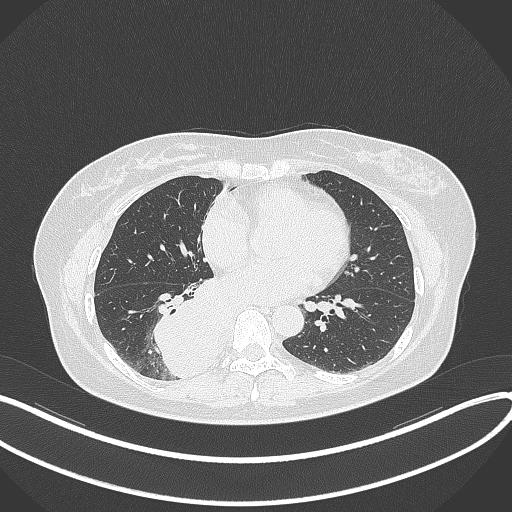
Chest CT, one axial slice. Position 152 of 331 along the scan axis. 120 kVp. Lung window (W 1500 / L -600 HU). 512 × 512 image matrix, field of view 400 × 400 mm. Patient: female, 54 years. From the clinical record (not read from this slice): clinical TNM (as recorded): T4 N0 M0.
Outlined on this slice (bounding box drawn by a radiologist):
- lung tumour (recorded histology: adenocarcinoma): bounding box [x1, y1, x2, y2] px = [148, 276, 228, 378]